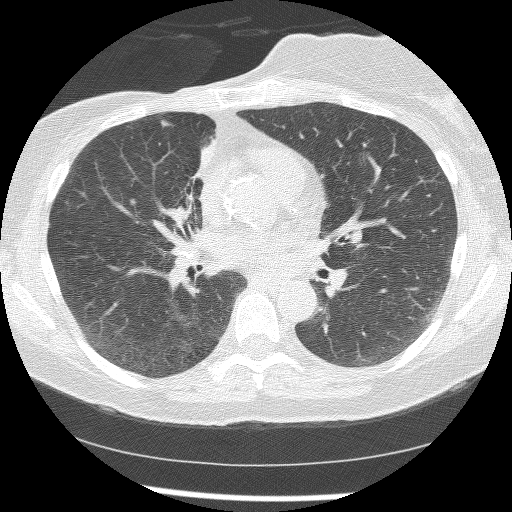
Axial slice from a low-dose chest CT screening exam, baseline annual screen, lung window (W 1500 / L -600 HU), lung (sharp) reconstruction kernel (BONE), 512 × 512 image matrix, field of view 315 × 315 mm. Female participant, aged 56 years at enrolment.
Expert-annotated lung lesion, bounding box [x1, y1, x2, y2] px = [151, 111, 180, 141]. The screening reader recorded 2 non-calcified nodules or masses ≥4 mm on this exam (right lower lobe, right middle lobe); which of them this box marks is not recorded. Official screen result: positive, change unspecified: nodule(s) >= 4 mm or enlarging nodule(s), mass(es), or other non-specific abnormalities suspicious for lung cancer. Later outcome: lung cancer diagnosed 1185 days after this screen (after the third annual screen) — adenocarcinoma, NOS, right upper lobe, stage IIIB (AJCC 6th edition), 8 mm at pathology.